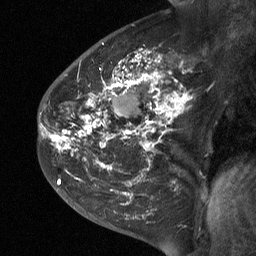
Breast MRI (dynamic contrast-enhanced), one sagittal slice. Position 36 of 64 along the scan axis. Dynamic contrast-enhanced study with each time point stored as its own series, time point 2 of 3 at this slice position (early post-contrast, ordered by acquisition time). 1.5 T. TE 4.8 ms, TR 27 ms. 2 mm slice thickness. 256 × 256 image matrix, field of view 200 × 200 mm. Patient: female, 42 years. From the clinical record (not read from this slice): setting: breast cancer imaged before/during neoadjuvant chemotherapy; receptor status: triple-negative.
Annotated regions visible in this slice (semi-automatic segmentation, software-assisted and operator-edited):
- analysis volume of interest (the breast-tissue region the enhancement analysis was run in; not a lesion): bounding box [x1, y1, x2, y2] px = [43, 29, 200, 190]
- tumour enhancement mask (voxels above the 90 % enhancement threshold inside the analysis volume of interest): [54, 51, 187, 184]